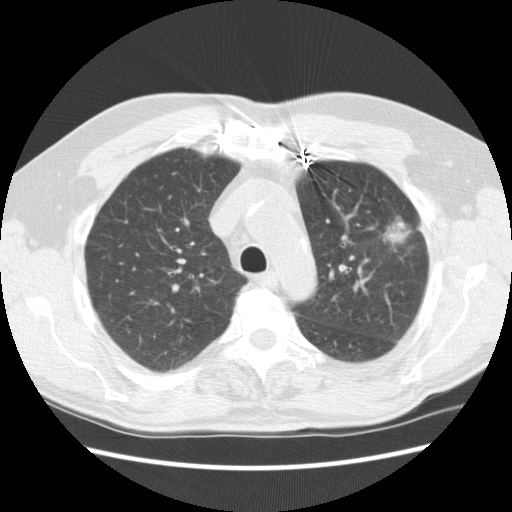
Chest CT (low-dose screening protocol), one axial image; baseline annual screen; lung window (W 1500 / L -600 HU); 2.5 mm slice thickness; standard (soft-tissue) reconstruction kernel (STANDARD); 512 × 512 image matrix, field of view 362 × 362 mm. Male participant, aged 72 years at enrolment. Former smoker at enrolment.
- Lesion marked by an expert reader, bounding box (x1, y1, x2, y2) in pixels: (346, 196, 429, 260).
- The exam's reader record, not a measurement of the box and not confirmed to be the same lesion: non-calcified nodule or mass ≥4 mm, left upper lobe, 25 × 18 mm, spiculated (stellate) margins, soft tissue attenuation.